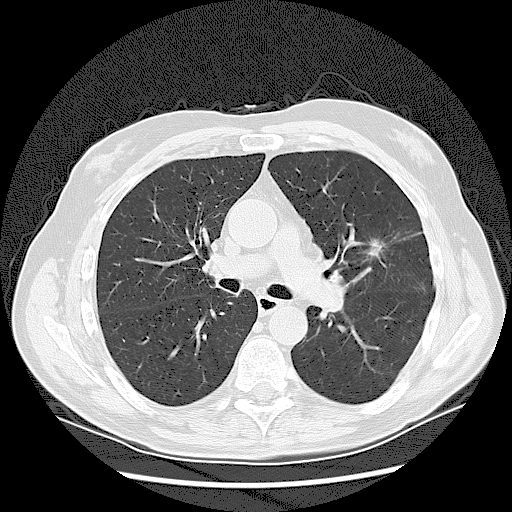
Axial slice from a low-dose chest CT screening exam; baseline screening round; lung window (W 1500 / L -600 HU); 120 kVp; slice 54 of 132 in the series; 512 × 512 image matrix, field of view 380 × 380 mm. Male, age 65 years at enrolment. Current smoker at enrolment.
Expert-annotated lung lesion, bounding box [x1, y1, x2, y2] px = [352, 230, 397, 273]. The exam's reader record, not a measurement of the box and not confirmed to be the same lesion: non-calcified nodule or mass ≥4 mm, left upper lobe, 37 × 27 mm, spiculated (stellate) margins, soft tissue attenuation. Later outcome: lung cancer diagnosed 56 days after this screen — non-small cell carcinoma, poorly differentiated (G3), stage IA (AJCC 6th edition).